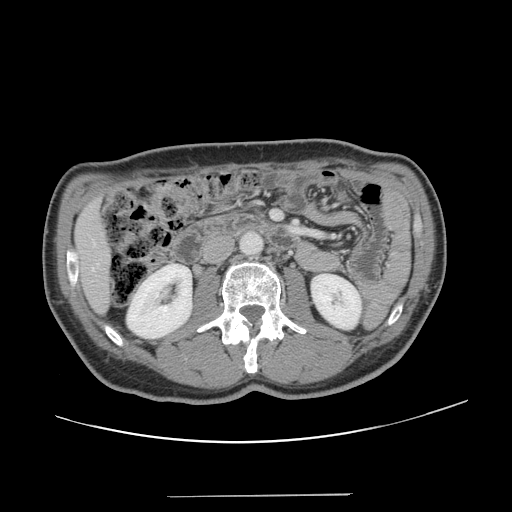
Contrast-enhanced abdominal CT, one axial slice; slice 50 of 131 in the series (ordered by position); 120 kVp; intravenous contrast given; soft-tissue window (W 400 / L 40 HU); 2.5 mm slice thickness; 512 × 512 image matrix, field of view 403 × 403 mm. Male patient, age 60 years. From the clinical record (not read from this slice): diagnosis: colorectal cancer liver metastases, imaged before liver resection; multiple liver metastases: no; largest metastasis: 2.5 cm; chemotherapy before resection: no.
Structures marked on this image (outlined manually by an expert reader):
- liver: box from (x=77, y=203) to (x=110, y=311) px
- planned liver remnant (the part of the liver to remain after resection): (x=77, y=203)–(x=109, y=311)